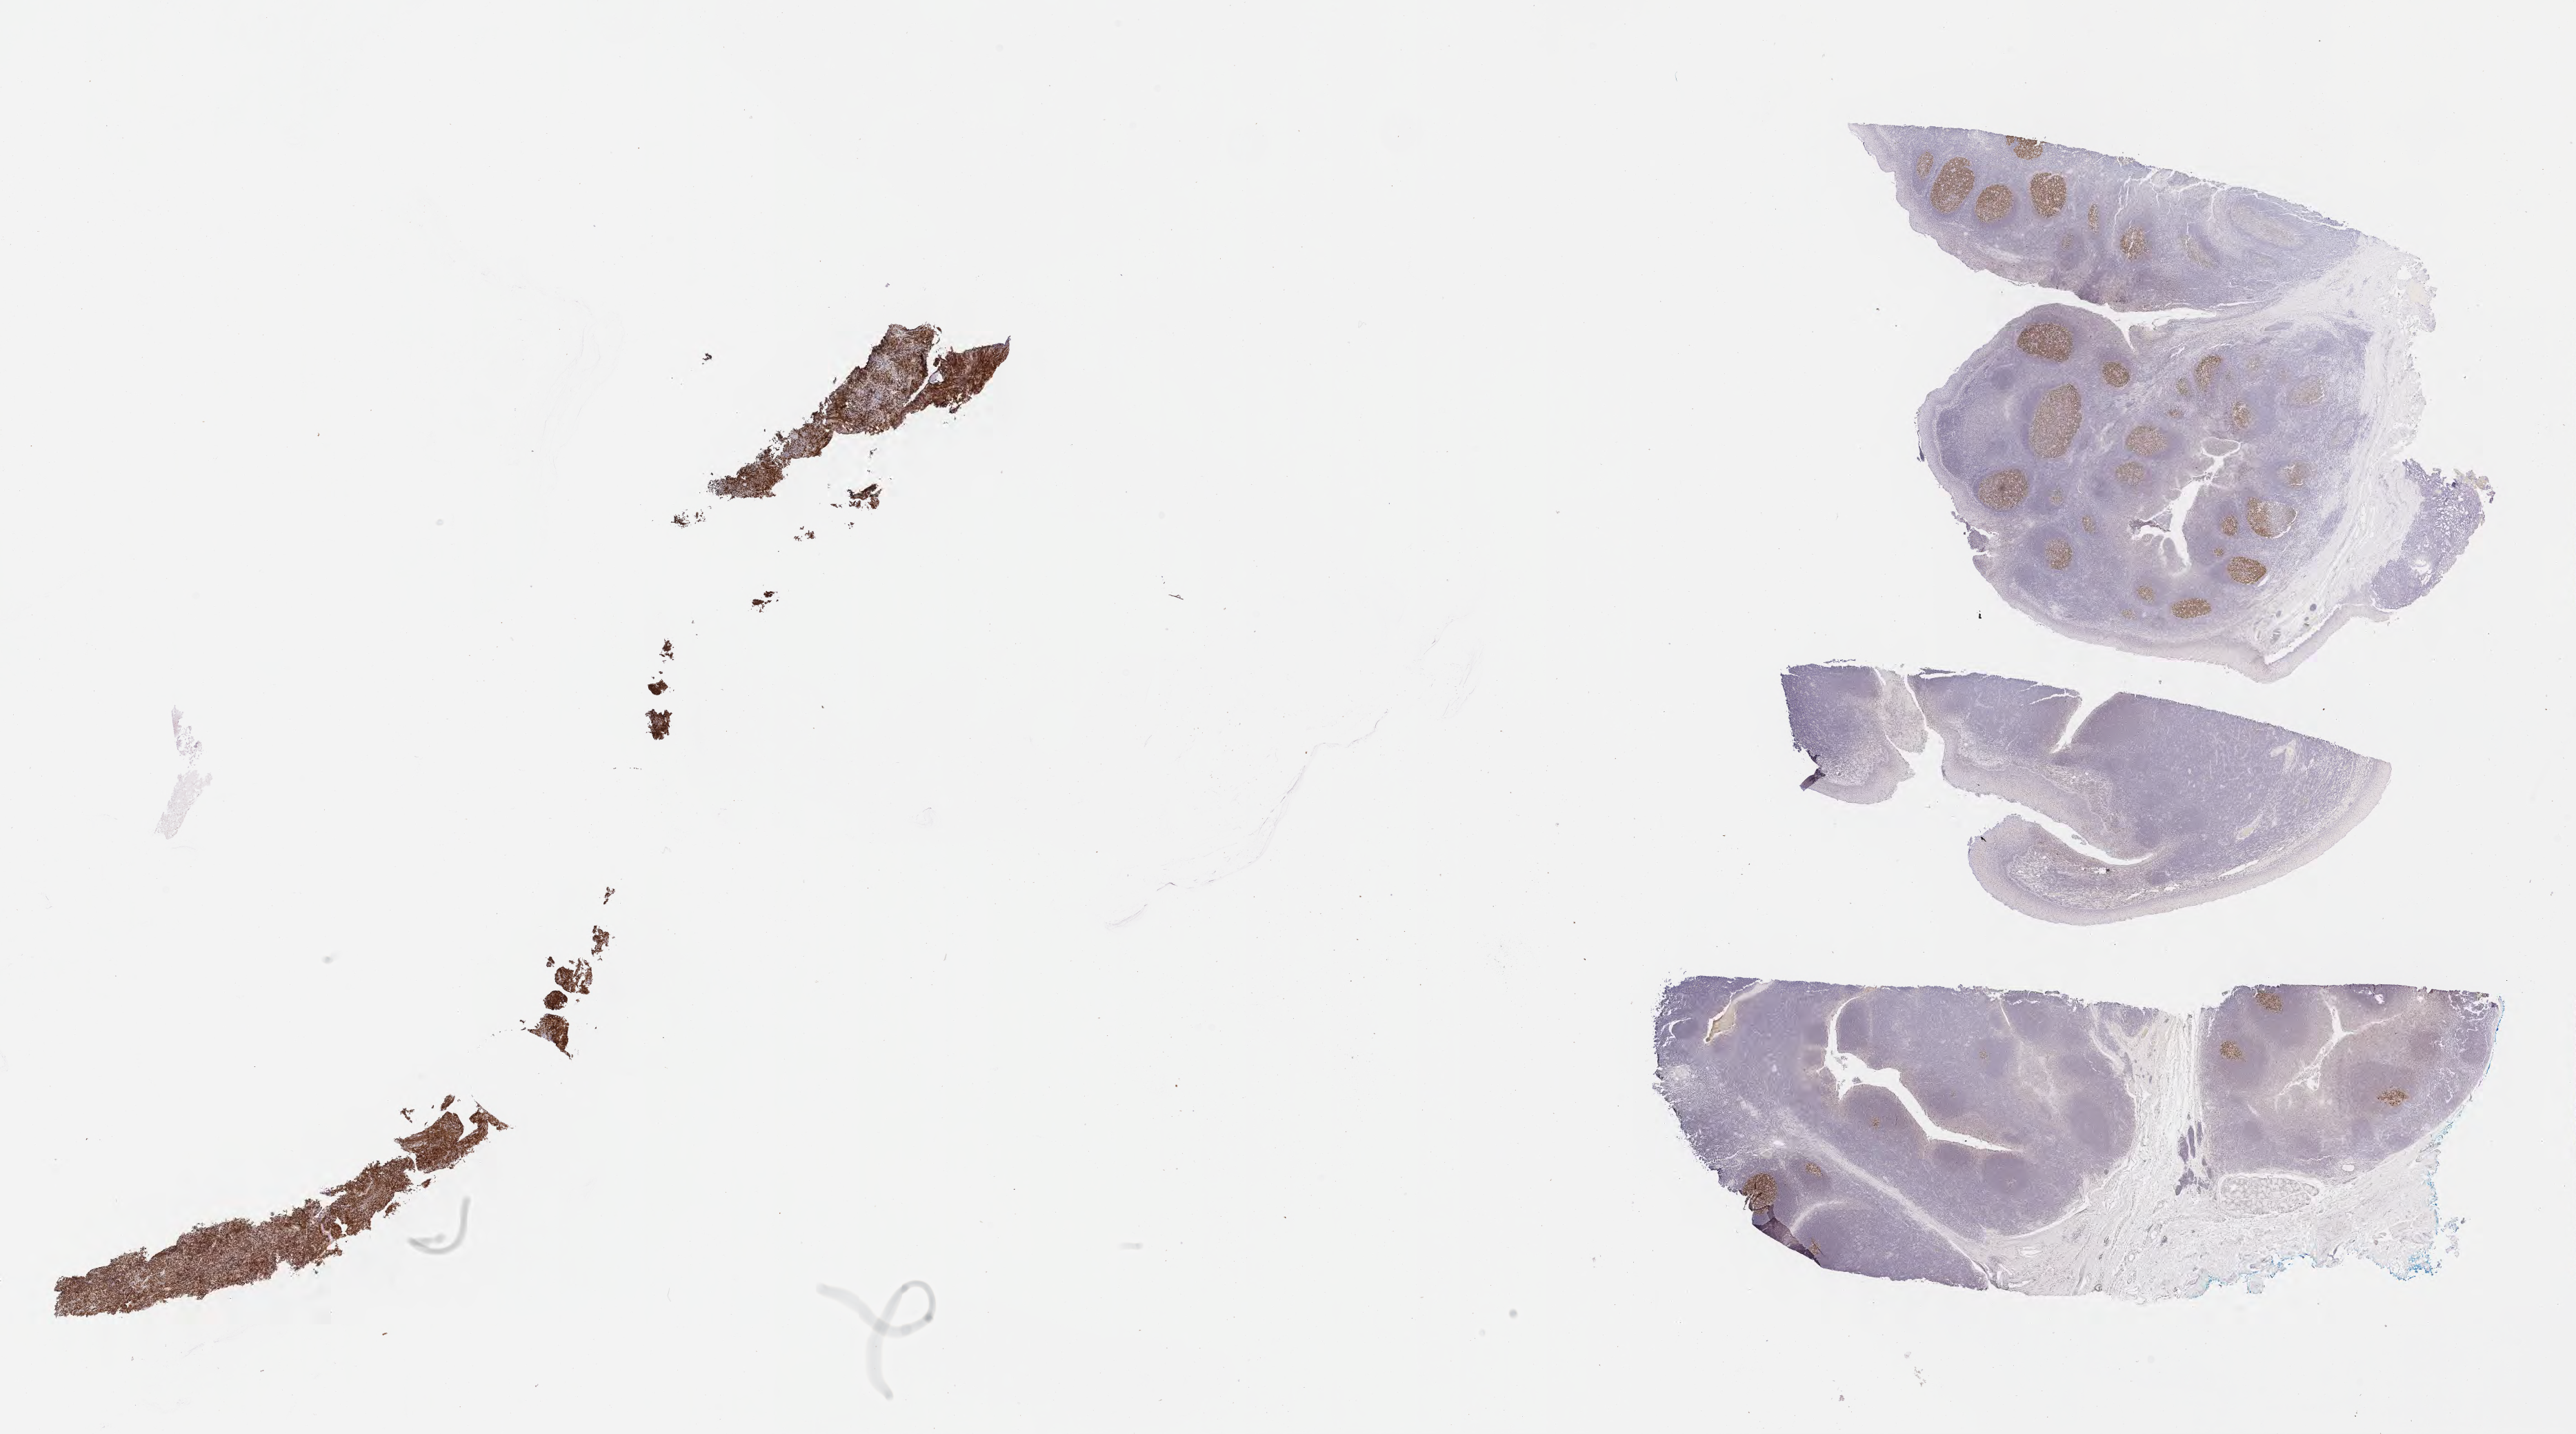
Whole-slide image, immunohistochemical stain for BCL6 — shown as a low-resolution overview of the whole scanned area (about 30.2 x 16.8 mm), specimen: tumor tissue, site: cranium. Patient: female, age at initial diagnosis 7 years.
Diagnosis: Burkitt lymphoma, NOS.